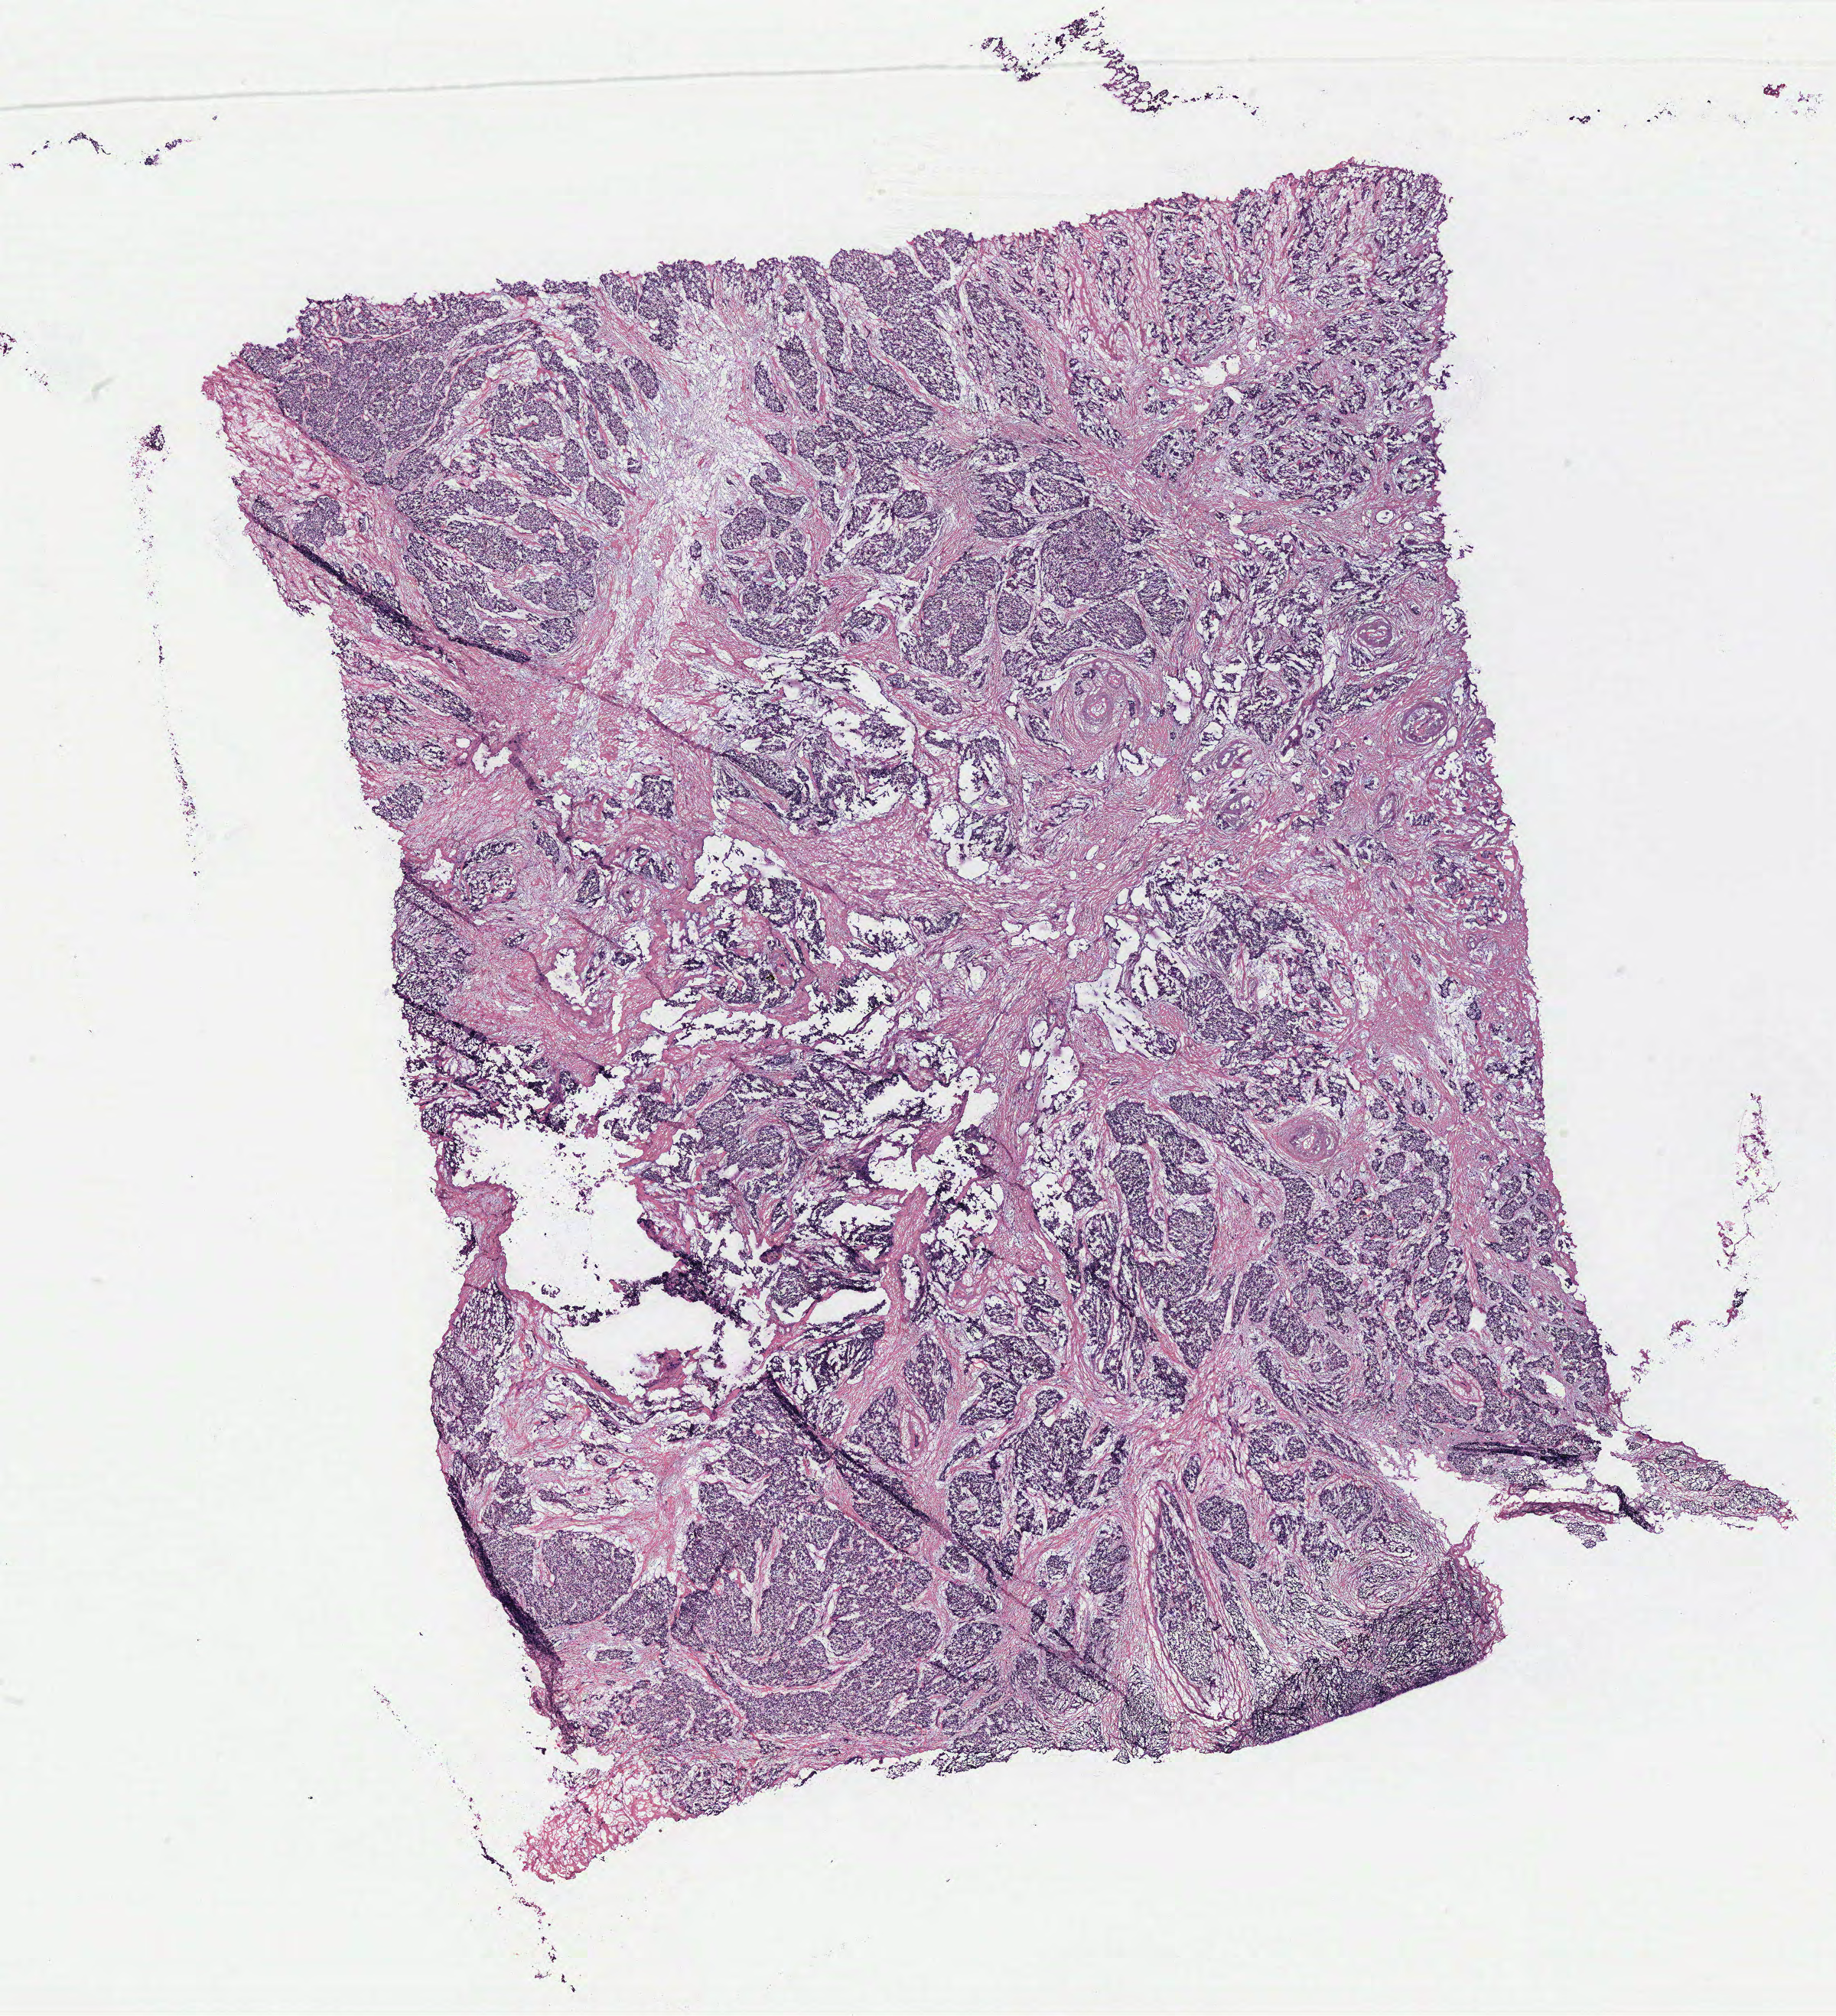
Whole-slide histology image, H&E, whole scanned area (about 19.2 x 21.1 mm, slide scanned at 40x) shown as a low-resolution overview, tumour tissue sample, breast. Female, 77 y/o.
- histologic diagnosis: Infiltrating duct carcinoma, NOS
- AJCC pathologic stage: IIA